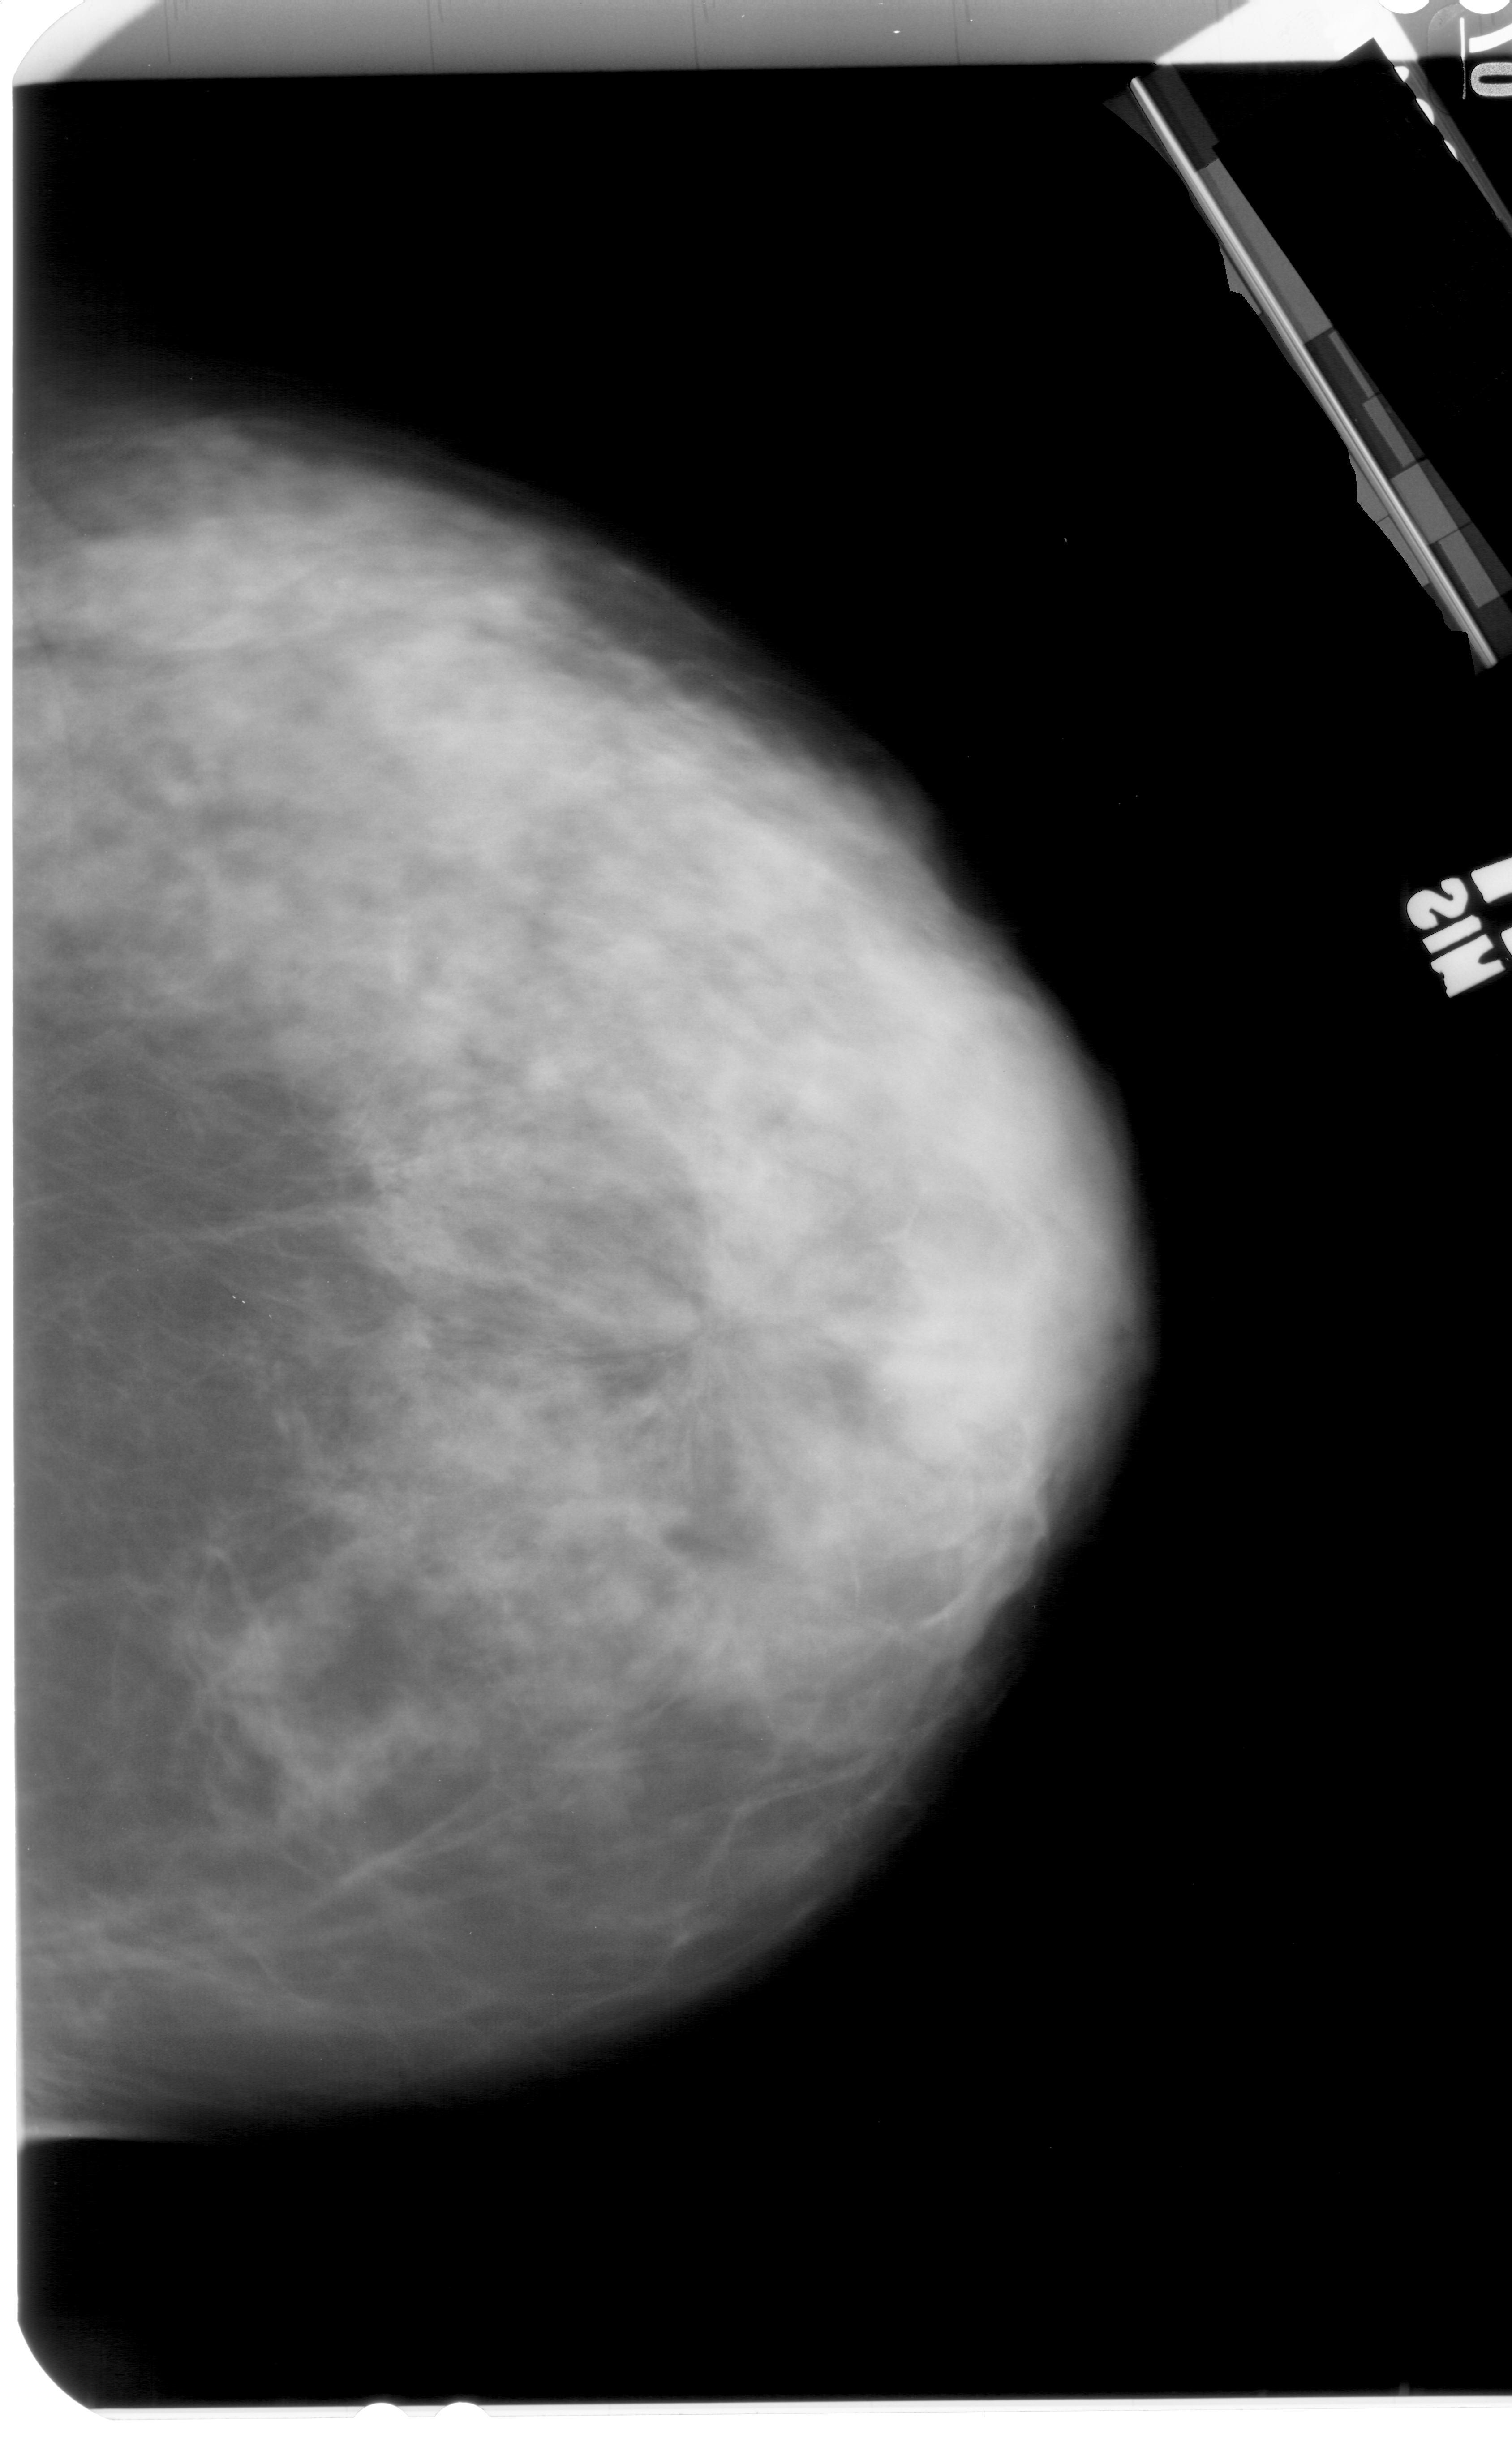
Mammogram (digitized film); right breast; craniocaudal (CC) view; breast composition: extremely dense (BI-RADS density category 4 of 4); 1512 × 2460 image matrix.
Expert-marked regions of interest on this film, with their recorded descriptors:
- mass, shape architectural distortion, margins spiculated; BI-RADS assessment category 5; subtlety rating 3 on a 1 (subtle) to 5 (obvious) scale; pathology result (as recorded, not read from the image): malignant: bounding box <571,1232,822,1408> (left, top, right, bottom; pixels)